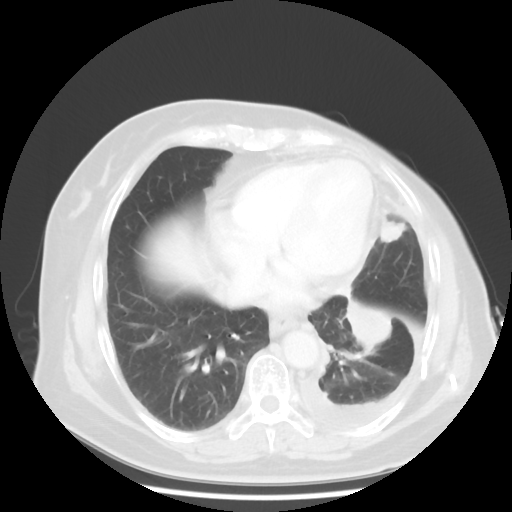
Chest CT, one axial slice; reconstruction kernel STANDARD; 120 kVp; lung window (W 1500 / L -600 HU); 5 mm slice thickness; 512 × 512 image matrix. Female patient, age 63 years. From the clinical record (not read from this slice): clinical TNM (as recorded): T2 N0 M1.
Structures marked on this image (rectangle marked by the reading radiologist):
- lung tumour (recorded histology: adenocarcinoma): box from (x=339, y=294) to (x=392, y=353) px